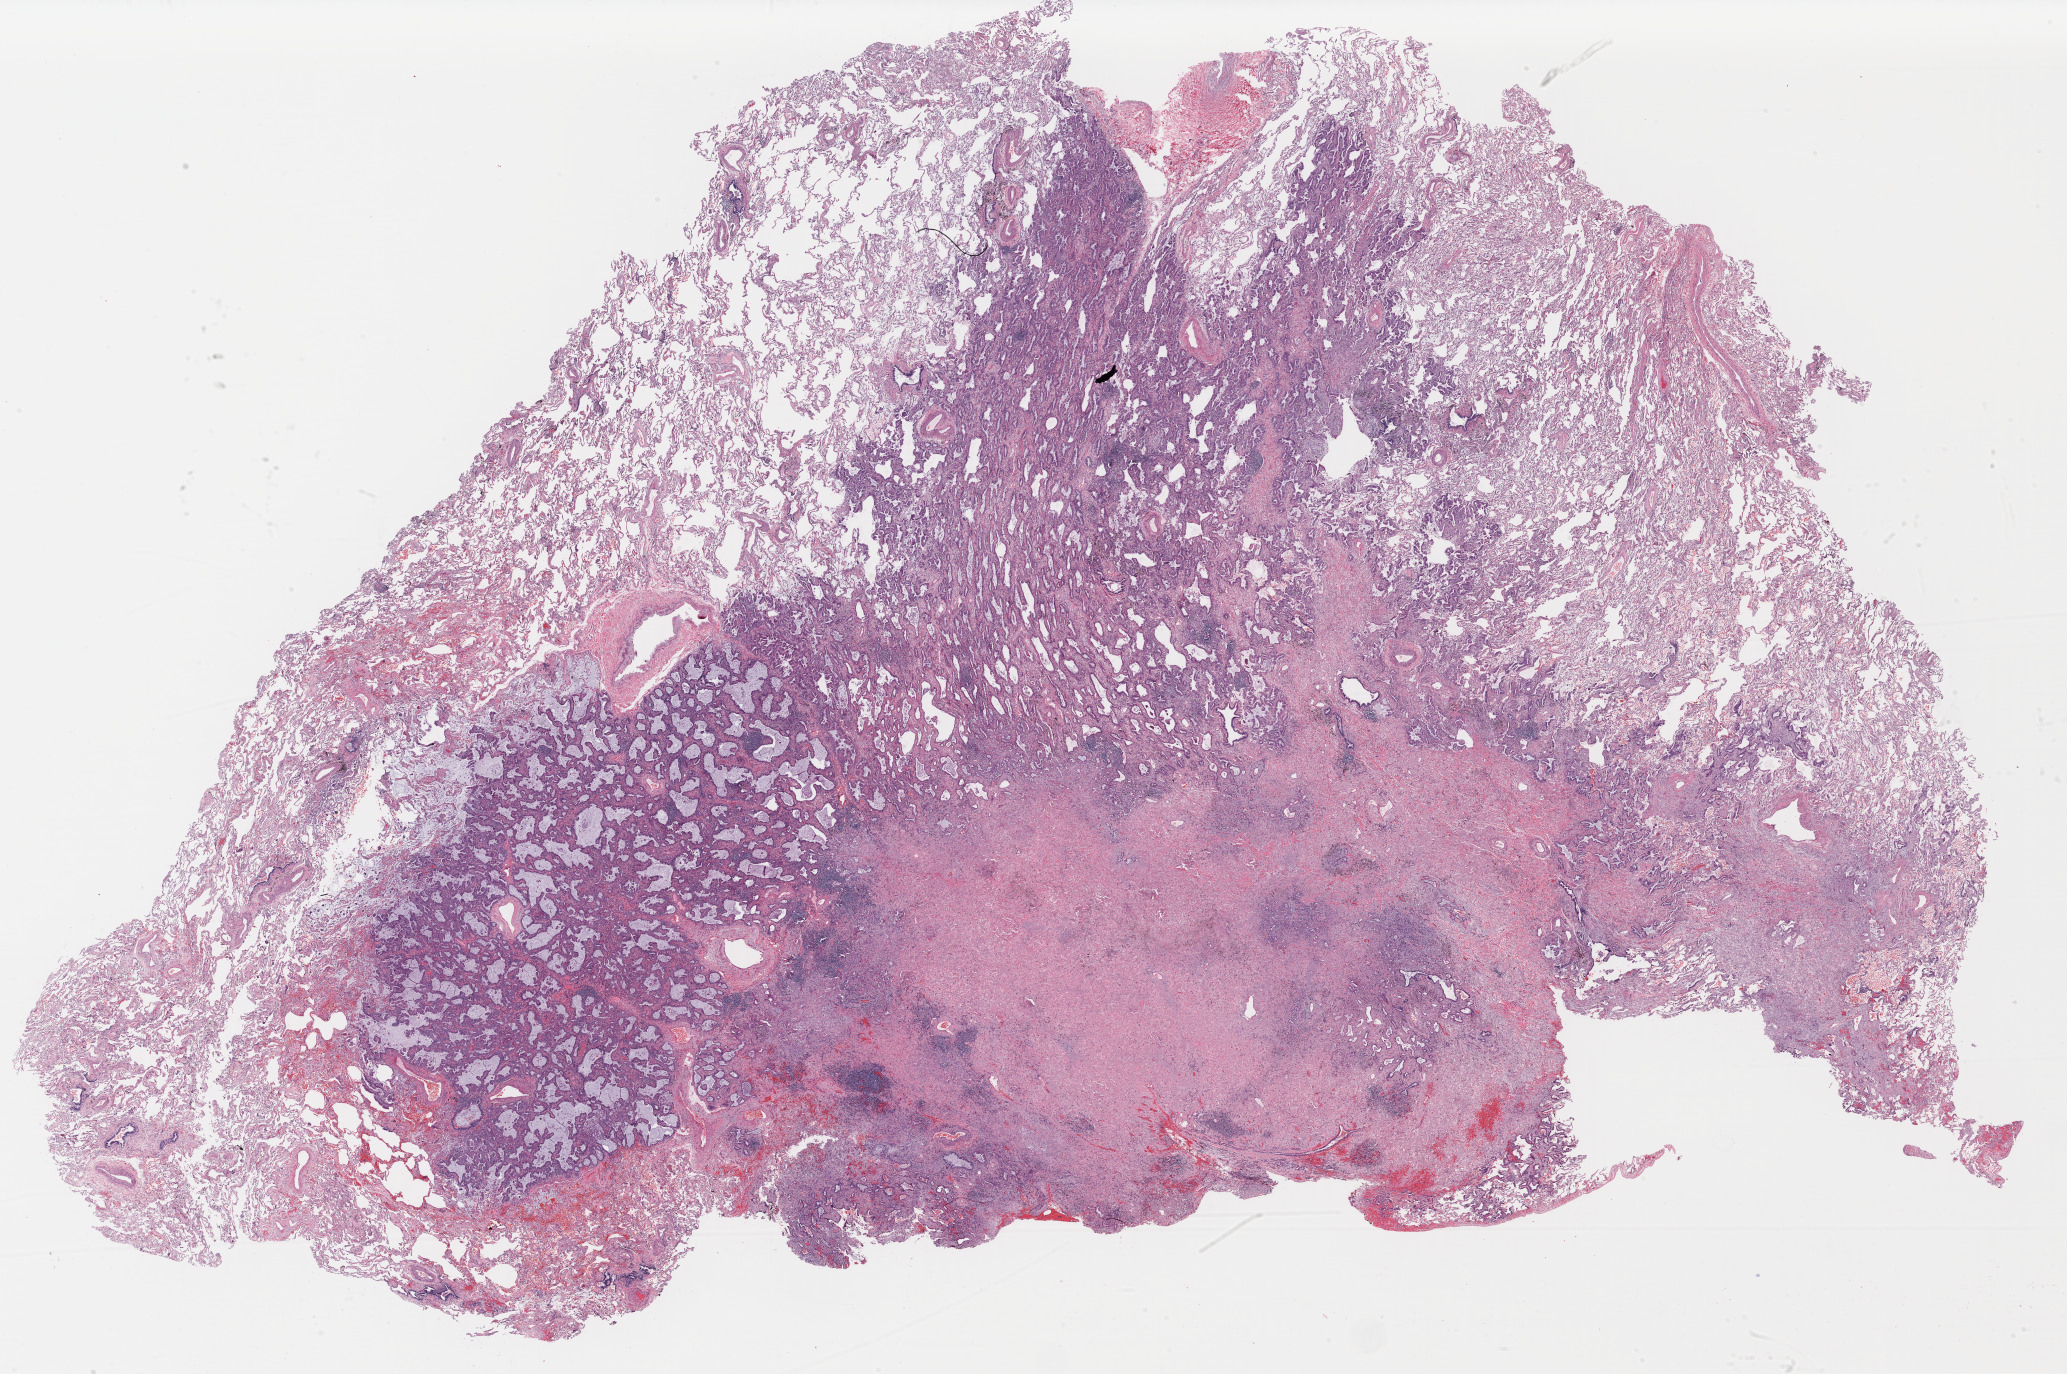
H&E whole-slide image — shown as a low-resolution overview of the whole scanned area (about 32.5 x 21.6 mm, acquisition: 40x scan). Formalin-fixed paraffin-embedded (FFPE) diagnostic section. Primary tumour sample from the lung. Female, age 72 years at initial diagnosis.
Laterality: left. Pathologic diagnosis: Acinar cell carcinoma (upper lobe, lung). AJCC pathologic stage: IA (7th edition).